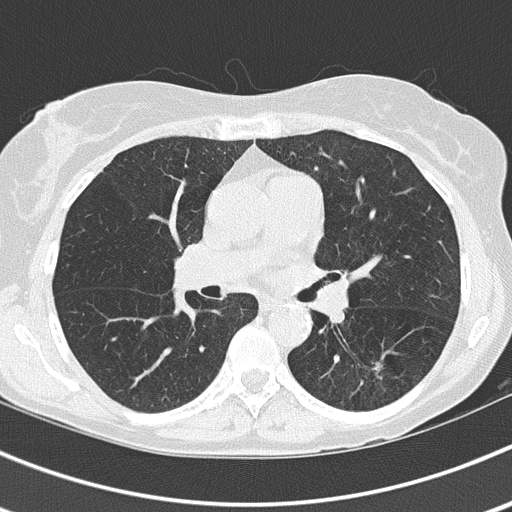
Axial slice from a low-dose chest CT screening exam, first (baseline) screen, lung window (W 1500 / L -600 HU), slice 68 of 143 in the series, 512 × 512 image matrix. Female, age 60 years at enrolment.
• Expert-annotated lung lesion, bounding box <357,355,387,386> (left, top, right, bottom; pixels).
• Screening reader's record for this exam: no non-calcified nodule ≥4 mm recorded.
• Official screen result: negative screen, no significant abnormalities.
• Participant outcome: lung cancer diagnosed 403 days after this screen — adenocarcinoma, NOS, left lower lobe, well differentiated (G1), stage IA (AJCC 6th edition), 15 mm at pathology.